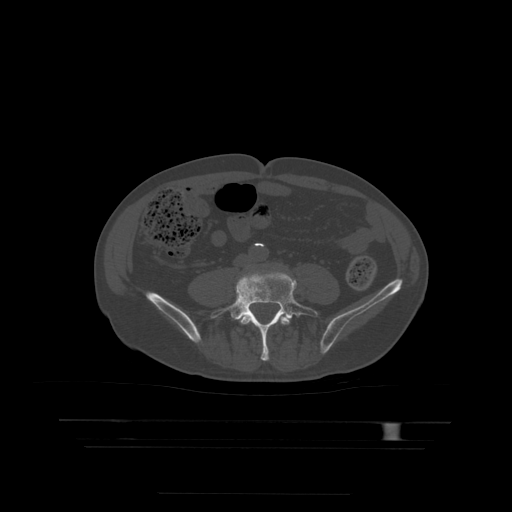
CT including the spine, one axial slice. Position 79 of 522 along the scan axis. Bone window (W 1800 / L 400 HU). 1.25 mm slice thickness. 512 × 512 image matrix. Patient age 68 years. Case-level facts recorded for this patient, not image findings: primary cancer: urothelial.
Structures marked on this image (semi-automatically segmented with operator editing):
- L4 vertebra: bounding box (x1, y1, x2, y2) in pixels: (240, 315, 290, 325)
- L5 vertebra: (211, 273, 319, 361)